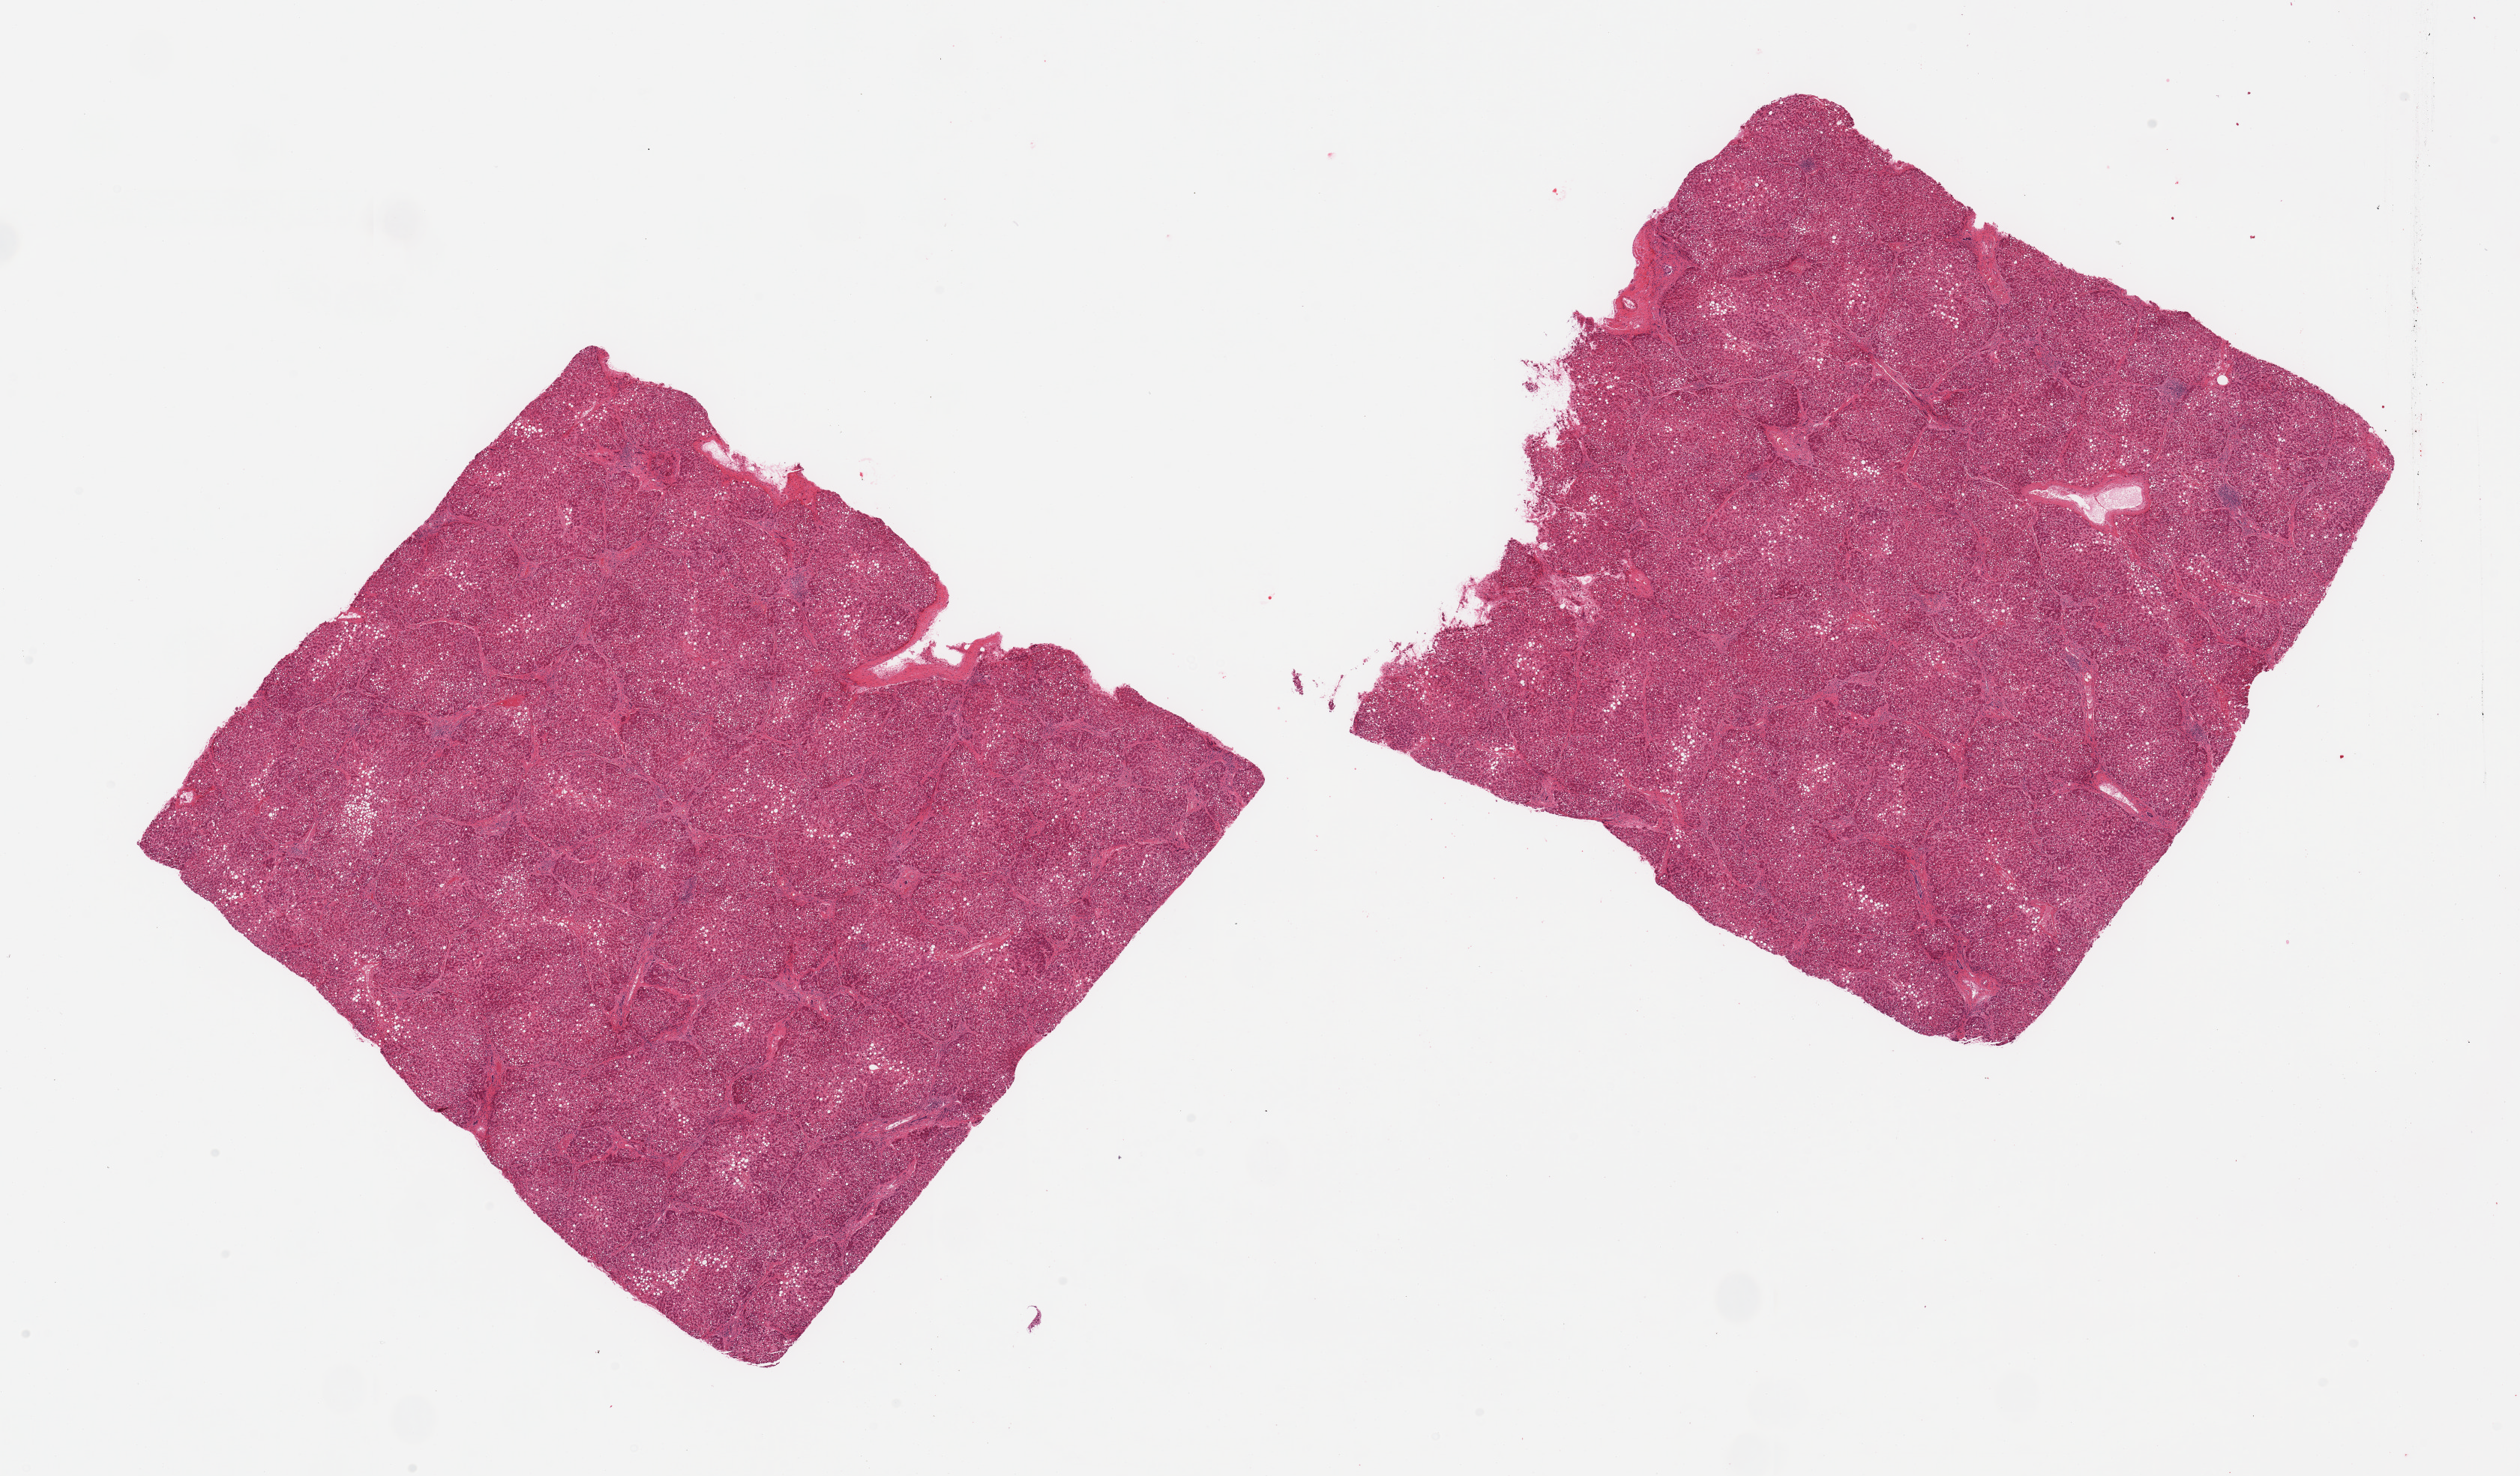
Digitized H&E-stained section, brightfield — a low-resolution overview of the entire scanned area, about 26.6 x 15.6 mm, PAXgene-fixed paraffin-embedded (PFPE) section, sampled site (target tissue): liver, tissue donor sample. Donor sex: male.
- pathologist's review note for this sample: 2 pieces, moderate macrovesicular steatosis involving ~80% of parenchyma; severe bridging fibrosis